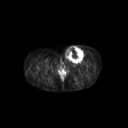
FDG PET of an extremity soft-tissue mass (from a PET/CT study), one axial slice; 3.27 mm slice thickness; 128 × 128 image matrix, field of view 600 × 600 mm. Patient: female, 24 years. Case-level facts recorded for this patient, not image findings: histological type: leiomyosarcoma; grade: high; site of the primary tumour: groin.
Structures marked on this image (expert contour drawn on MRI and transferred to this co-registered scan by the dataset authors):
- gross tumour volume including surrounding oedema: bounding box [x1, y1, x2, y2] px = [63, 44, 87, 63]
- gross tumour volume (mass): [66, 45, 84, 62]